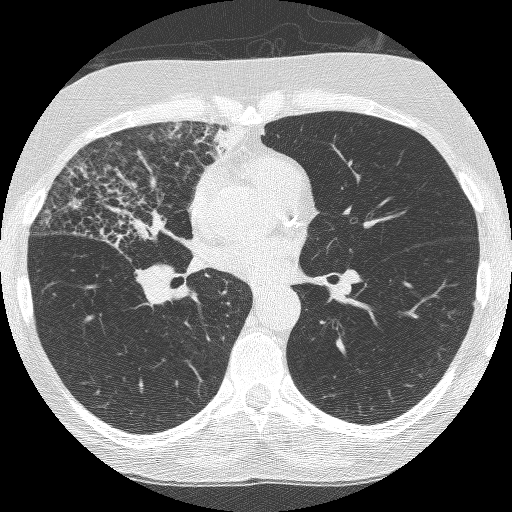
Axial slice from a low-dose chest CT screening exam; third annual screen; lung window (W 1500 / L -600 HU); lung (sharp) reconstruction kernel (BONE); slice 133 of 253 in the series. Female, age 64 years at enrolment. Former smoker at enrolment.
• Lesion marked by an expert reader, bounding box [x1, y1, x2, y2] px = [56, 162, 200, 308].
• Reader record for this screening exam (exam-level; its link to the box is not recorded): non-calcified nodule or mass ≥4 mm, right upper lobe, 49 × 43 mm, spiculated (stellate) margins, soft tissue attenuation, pre-existing on the prior screen: yes; interval growth: yes.
• Lung cancer was diagnosed 7 days after this screen: adenocarcinoma, NOS, right upper lobe, right middle lobe, right hilum, stage IV (AJCC 6th edition), 85 mm at pathology.